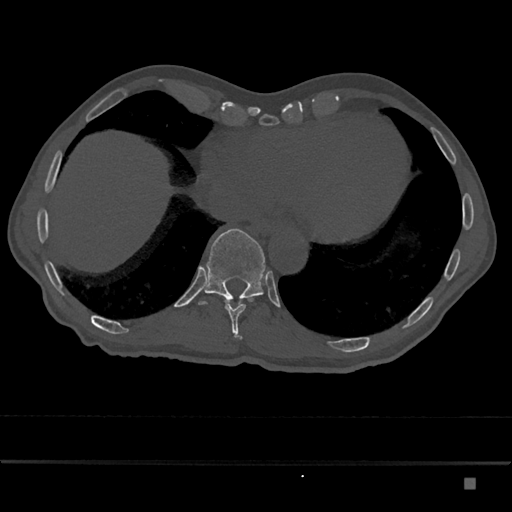
CT including the spine, one axial slice. Position 709 of 797 along the scan axis. Reconstruction kernel Br40s/3. 120 kVp. Bone window (W 1800 / L 400 HU). 0.5 mm slice thickness. 512 × 512 image matrix, field of view 390 × 390 mm. Patient: male, 72 years. From the clinical record (not read from this slice): primary cancer: prostate.
Structures marked on this image (semi-automatic segmentation, software-assisted and operator-edited):
- T10 vertebra: bounding box <225,297,252,339> (left, top, right, bottom; pixels)
- T11 vertebra: <198,228,266,305>